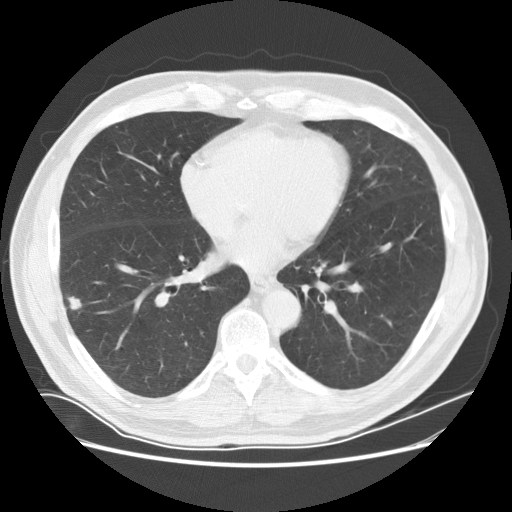
Chest CT (low-dose screening protocol), one axial image; first (baseline) screen; lung window (W 1500 / L -600 HU); 512 × 512 image matrix, field of view 380 × 380 mm. Male participant, aged 72 years at enrolment. Current smoker at enrolment.
Expert-annotated lung lesion, box from (x=57, y=291) to (x=92, y=323) px. Reader record for this screening exam (exam-level; its link to the box is not recorded): non-calcified nodule or mass ≥4 mm, right lower lobe, 13 × 8 mm, poorly defined margins, soft tissue attenuation. Official screen result: positive, change unspecified: nodule(s) >= 4 mm or enlarging nodule(s), mass(es), or other non-specific abnormalities suspicious for lung cancer. Later outcome: lung cancer diagnosed 17 days after this screen — non-small cell carcinoma, right lower lobe, moderately differentiated (G2), stage IA (AJCC 6th edition), 10 mm at pathology.